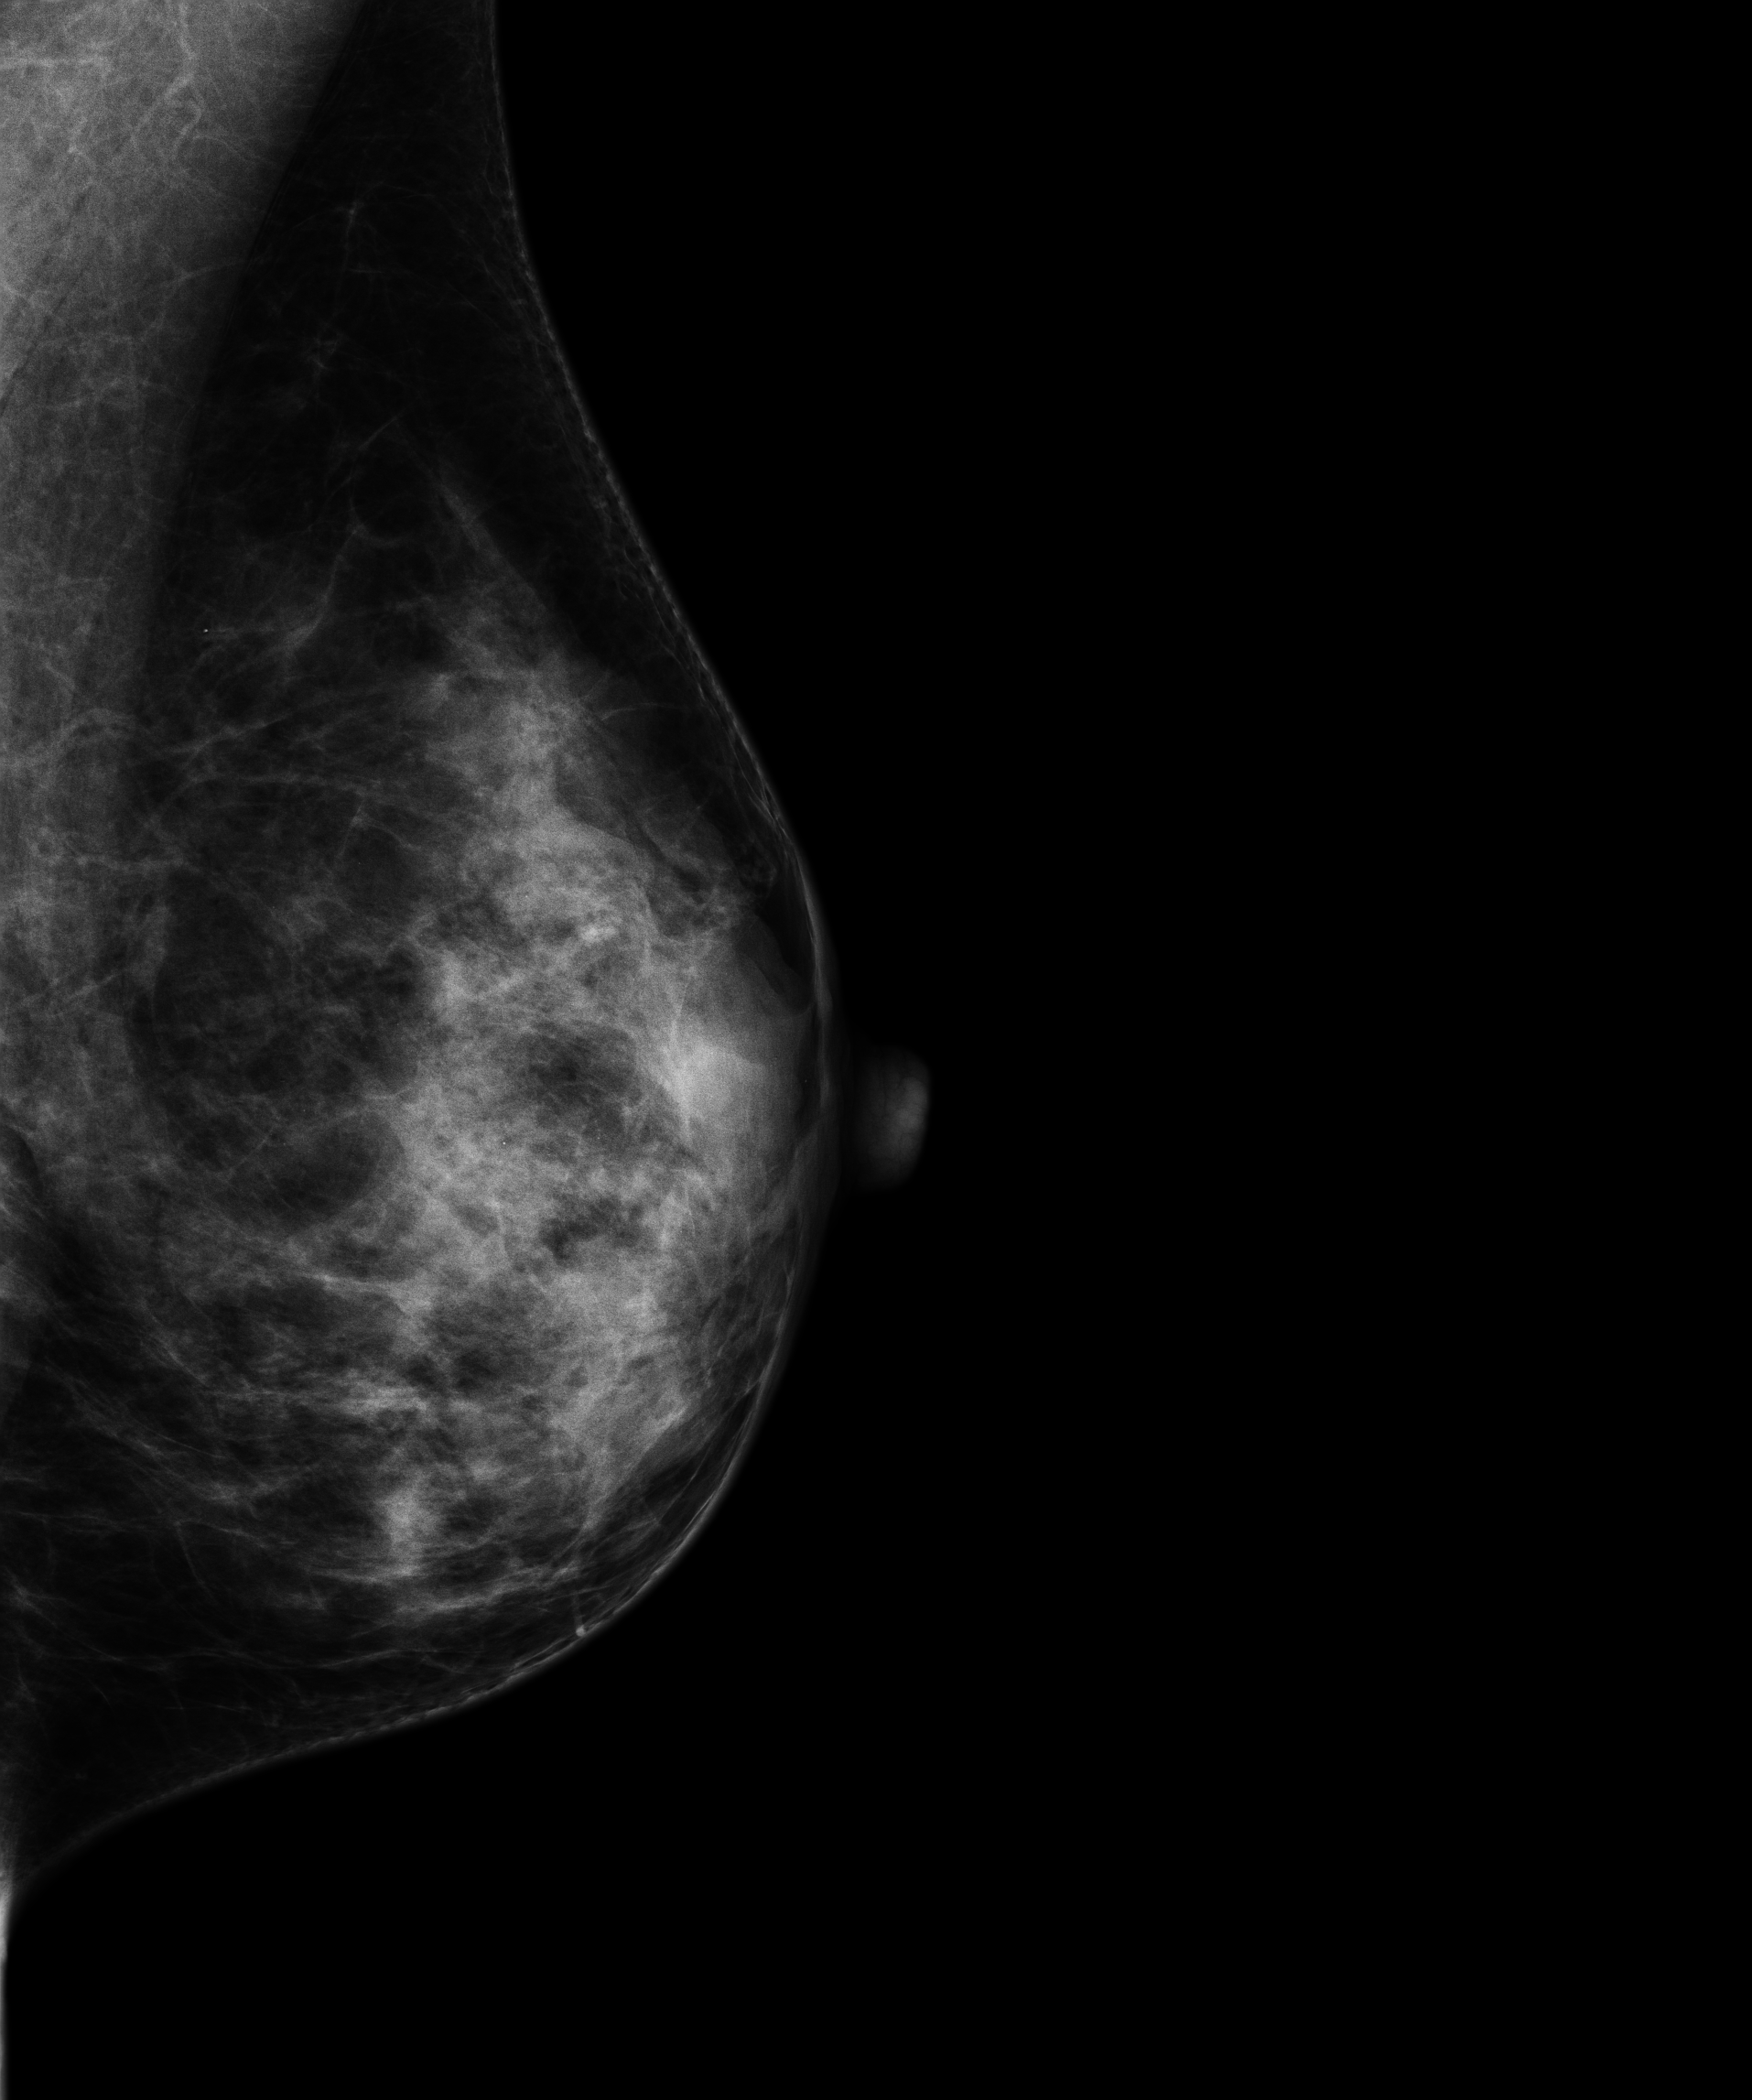
Screening examination. Patient: female, 56 years.
Image type: full-field digital mammogram. Breast: left. Projection: mediolateral oblique (MLO) view. Breast density at the screening exam (both breasts): extremely dense (BI-RADS density category d). Final BI-RADS category for the screening round (tomosynthesis exam, both breasts): category 1. Recall: no recall after this screen.